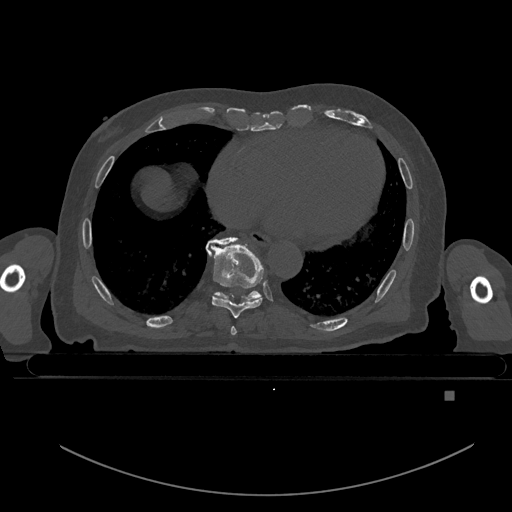
CT including the spine, one axial slice; slice 189 of 969 in the series (ordered by position); bone window (W 1800 / L 400 HU); 0.5 mm slice thickness; 512 × 512 image matrix. Male patient, age 82 years. From the clinical record (not read from this slice): primary cancer: prostate; vertebrae with lytic lesions (as recorded): T11, T9, T8, T2.
Outlined on this slice (semi-automatically segmented with operator editing):
- T7 vertebra: bounding box [x1, y1, x2, y2] px = [231, 326, 237, 335]
- T8 vertebra: [208, 239, 264, 318]
- T9 vertebra: [206, 237, 262, 301]